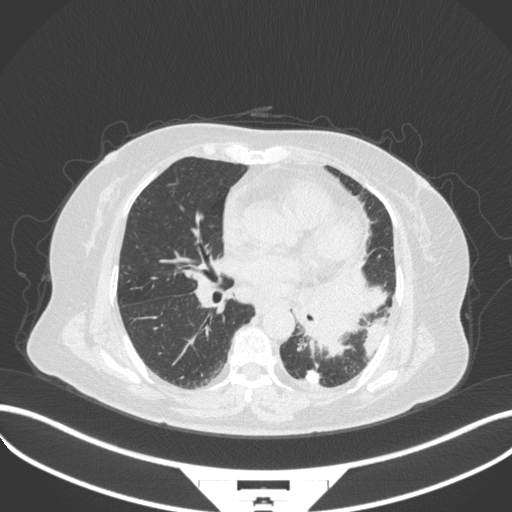
Chest CT, one axial slice; slice 168 of 328 in the series (ordered by position); reconstruction kernel B31f; lung window (W 1500 / L -600 HU); 1 mm slice thickness; 512 × 512 image matrix, field of view 400 × 400 mm. Patient: female, 69 years. From the clinical record (not read from this slice): clinical TNM (as recorded): T2b N3 M1.
Outlined on this slice (bounding box drawn by a radiologist):
- lung tumour (recorded histology: adenocarcinoma): bounding box (x1, y1, x2, y2) in pixels: (293, 265, 387, 361)